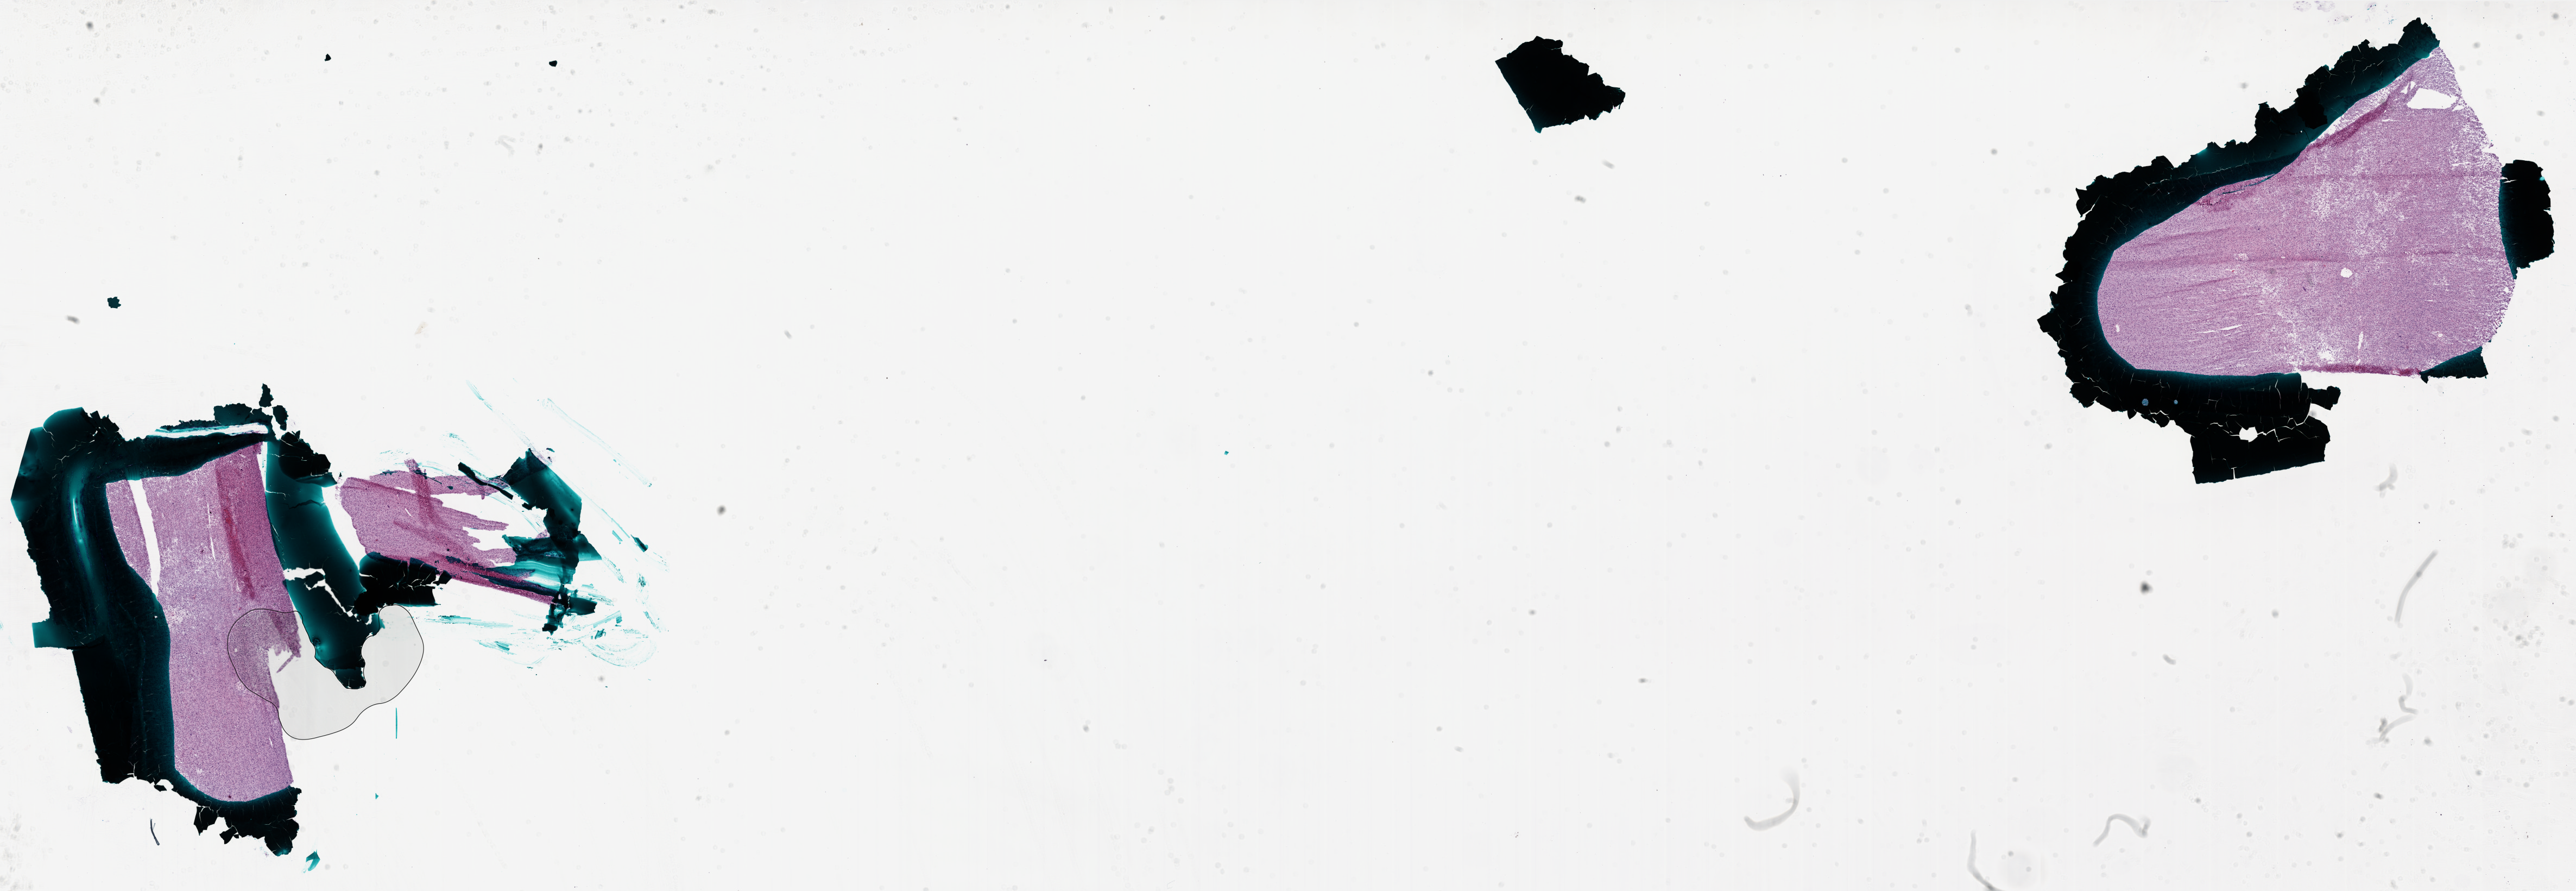
Whole-slide histology image, H&E-stained, a low-resolution overview of the entire scanned area, about 38.0 x 13.1 mm (from a 20x scan). Frozen section from the bottom of the tissue portion. Brain, primary tumour sample. Patient: male, age at initial diagnosis 63 years. Pathologist review of this section (percent, as recorded): tumour cells 95%, tumour nuclei 95%, normal cells 0%, stromal cells 5%, necrosis 0%.
* histologic diagnosis: Glioblastoma